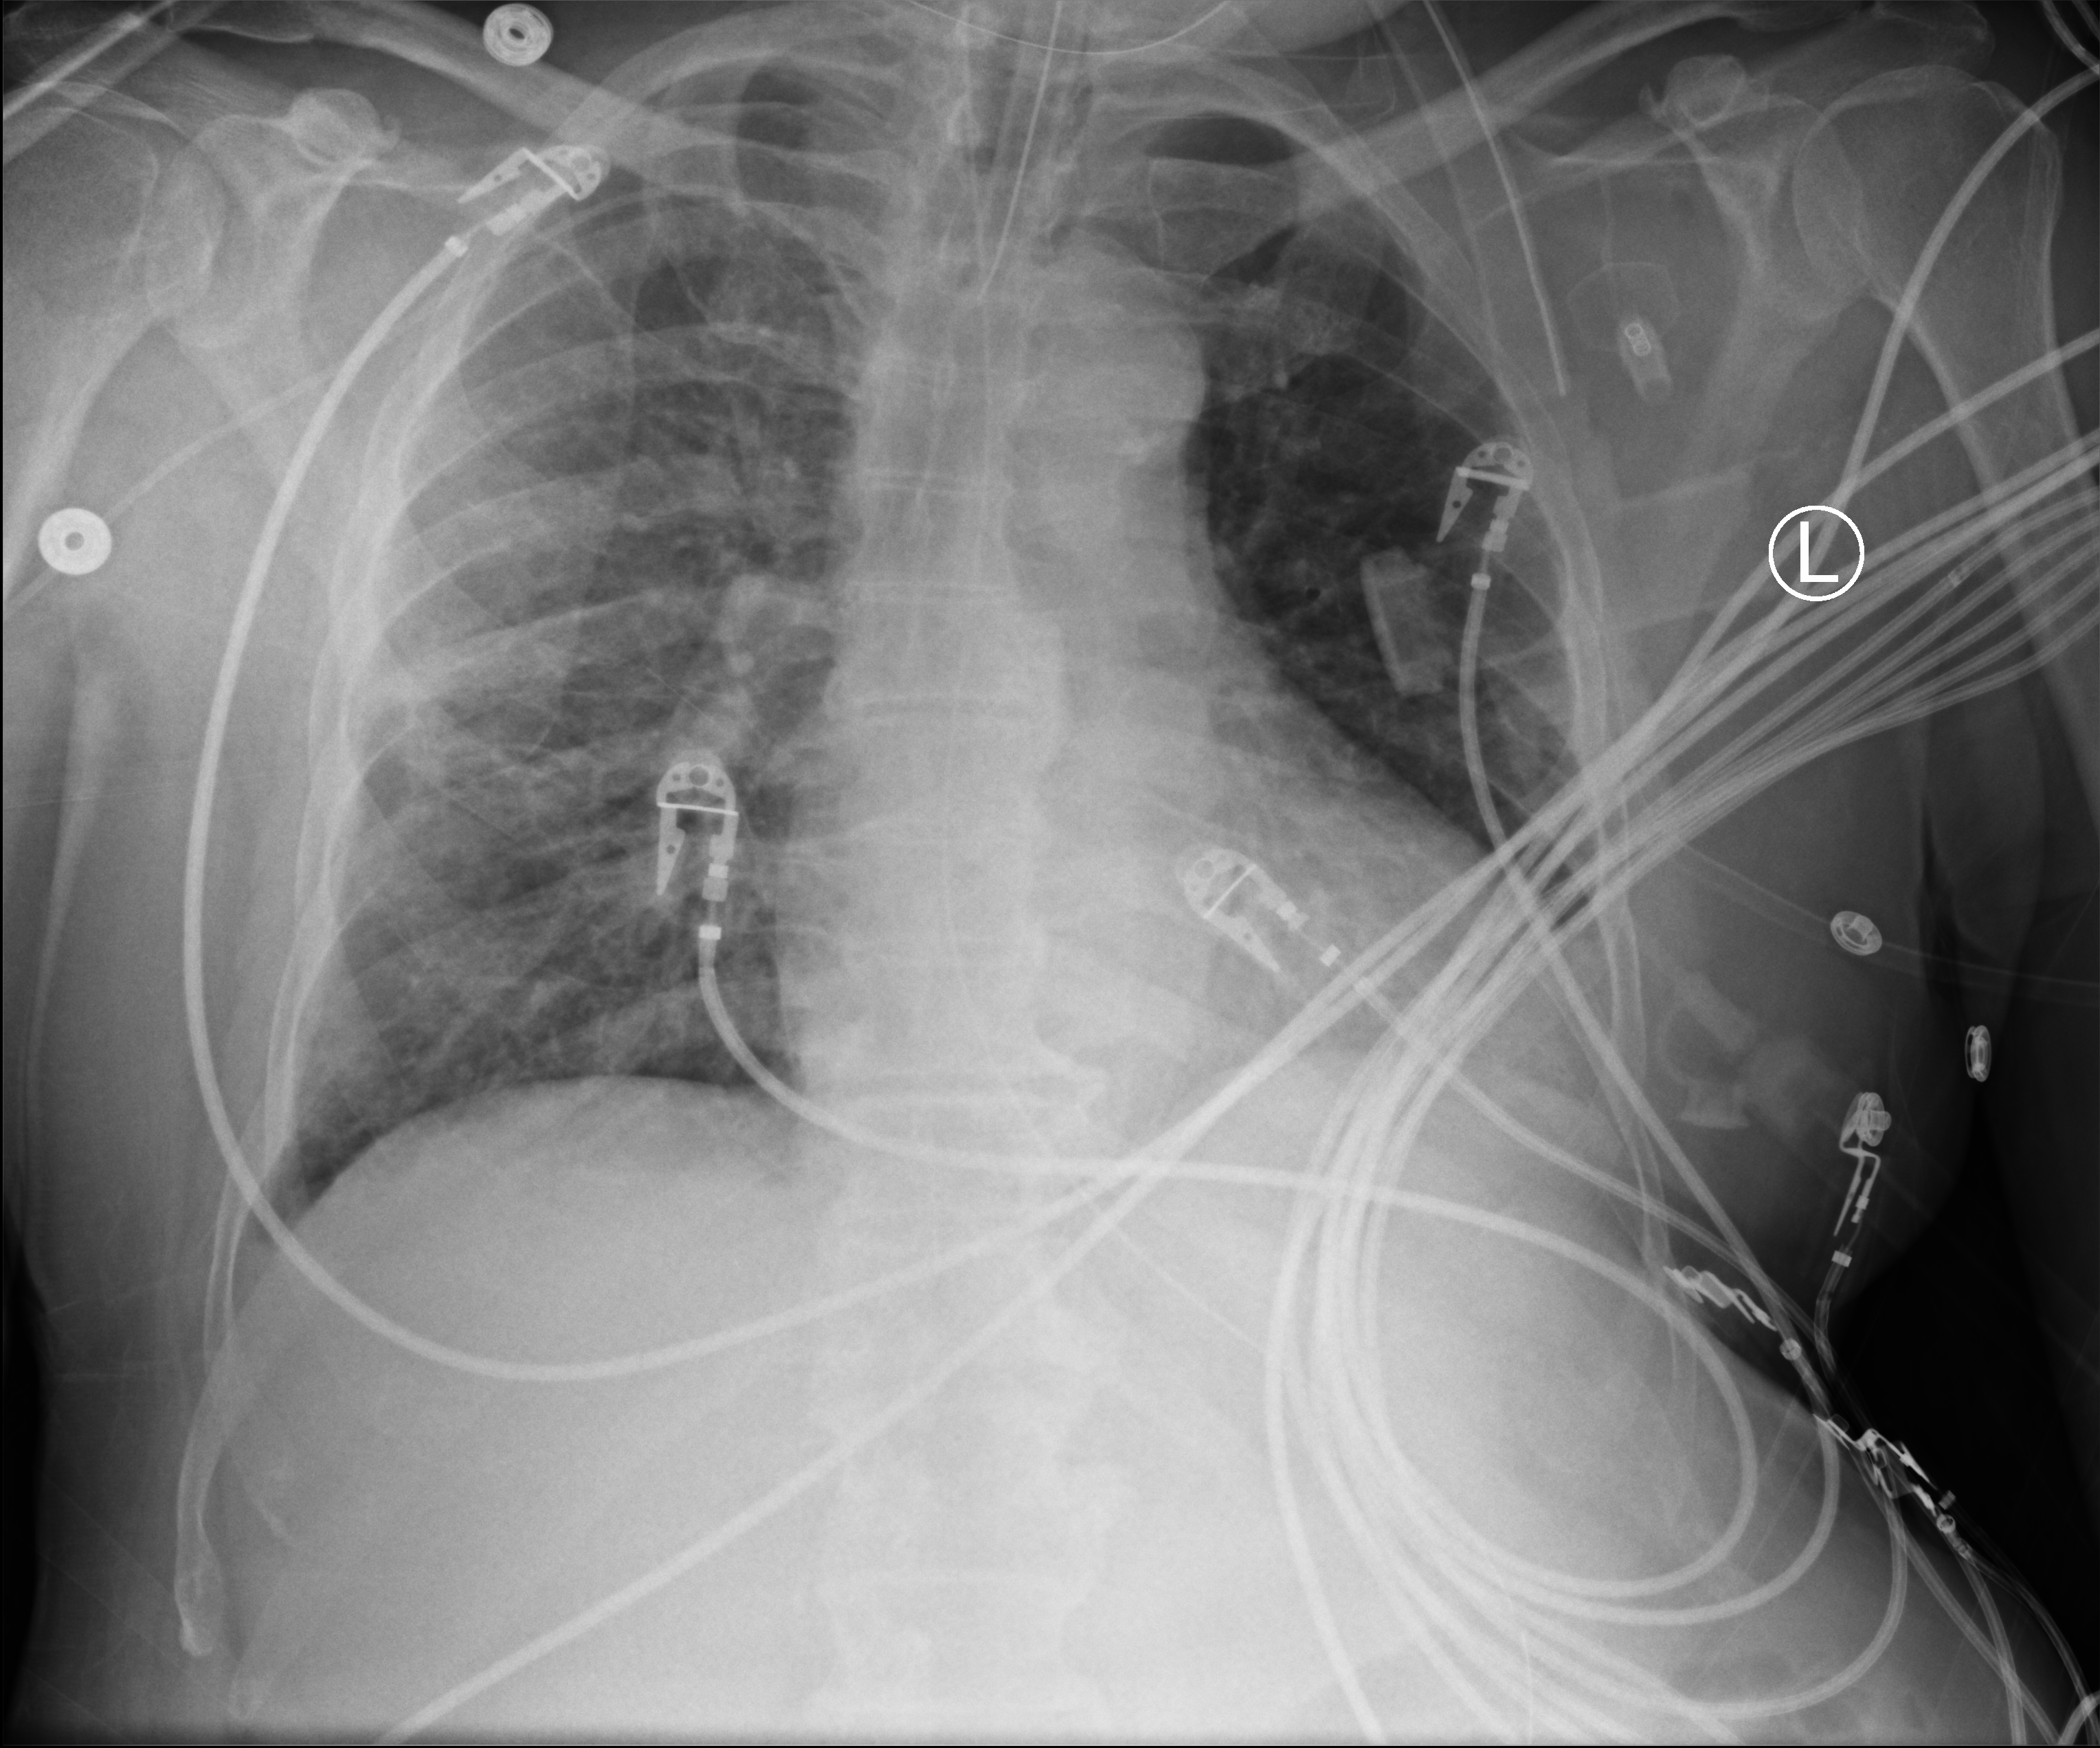
Chest X-ray (portable); anteroposterior (AP) projection. Patient hospitalised with COVID-19; male, aged 60–74 years.
From the hospital-stay record, not from the radiograph (when in the stay this image was taken is not recorded): mechanically ventilated during this hospital stay: yes.